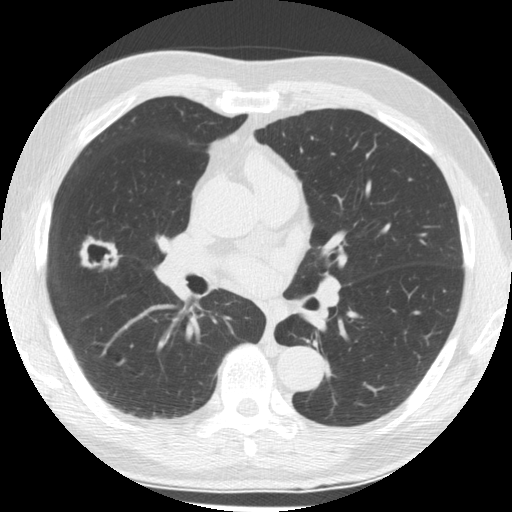
Low-dose screening chest CT, one axial slice. 120 kVp. Lung window (W 1500 / L -600 HU). 512 × 512 image matrix.
Annotated regions visible in this slice (manually delineated by an expert):
- lesion 1 (tumor, middle lobe of right lung): box from (x=80, y=236) to (x=122, y=269) px